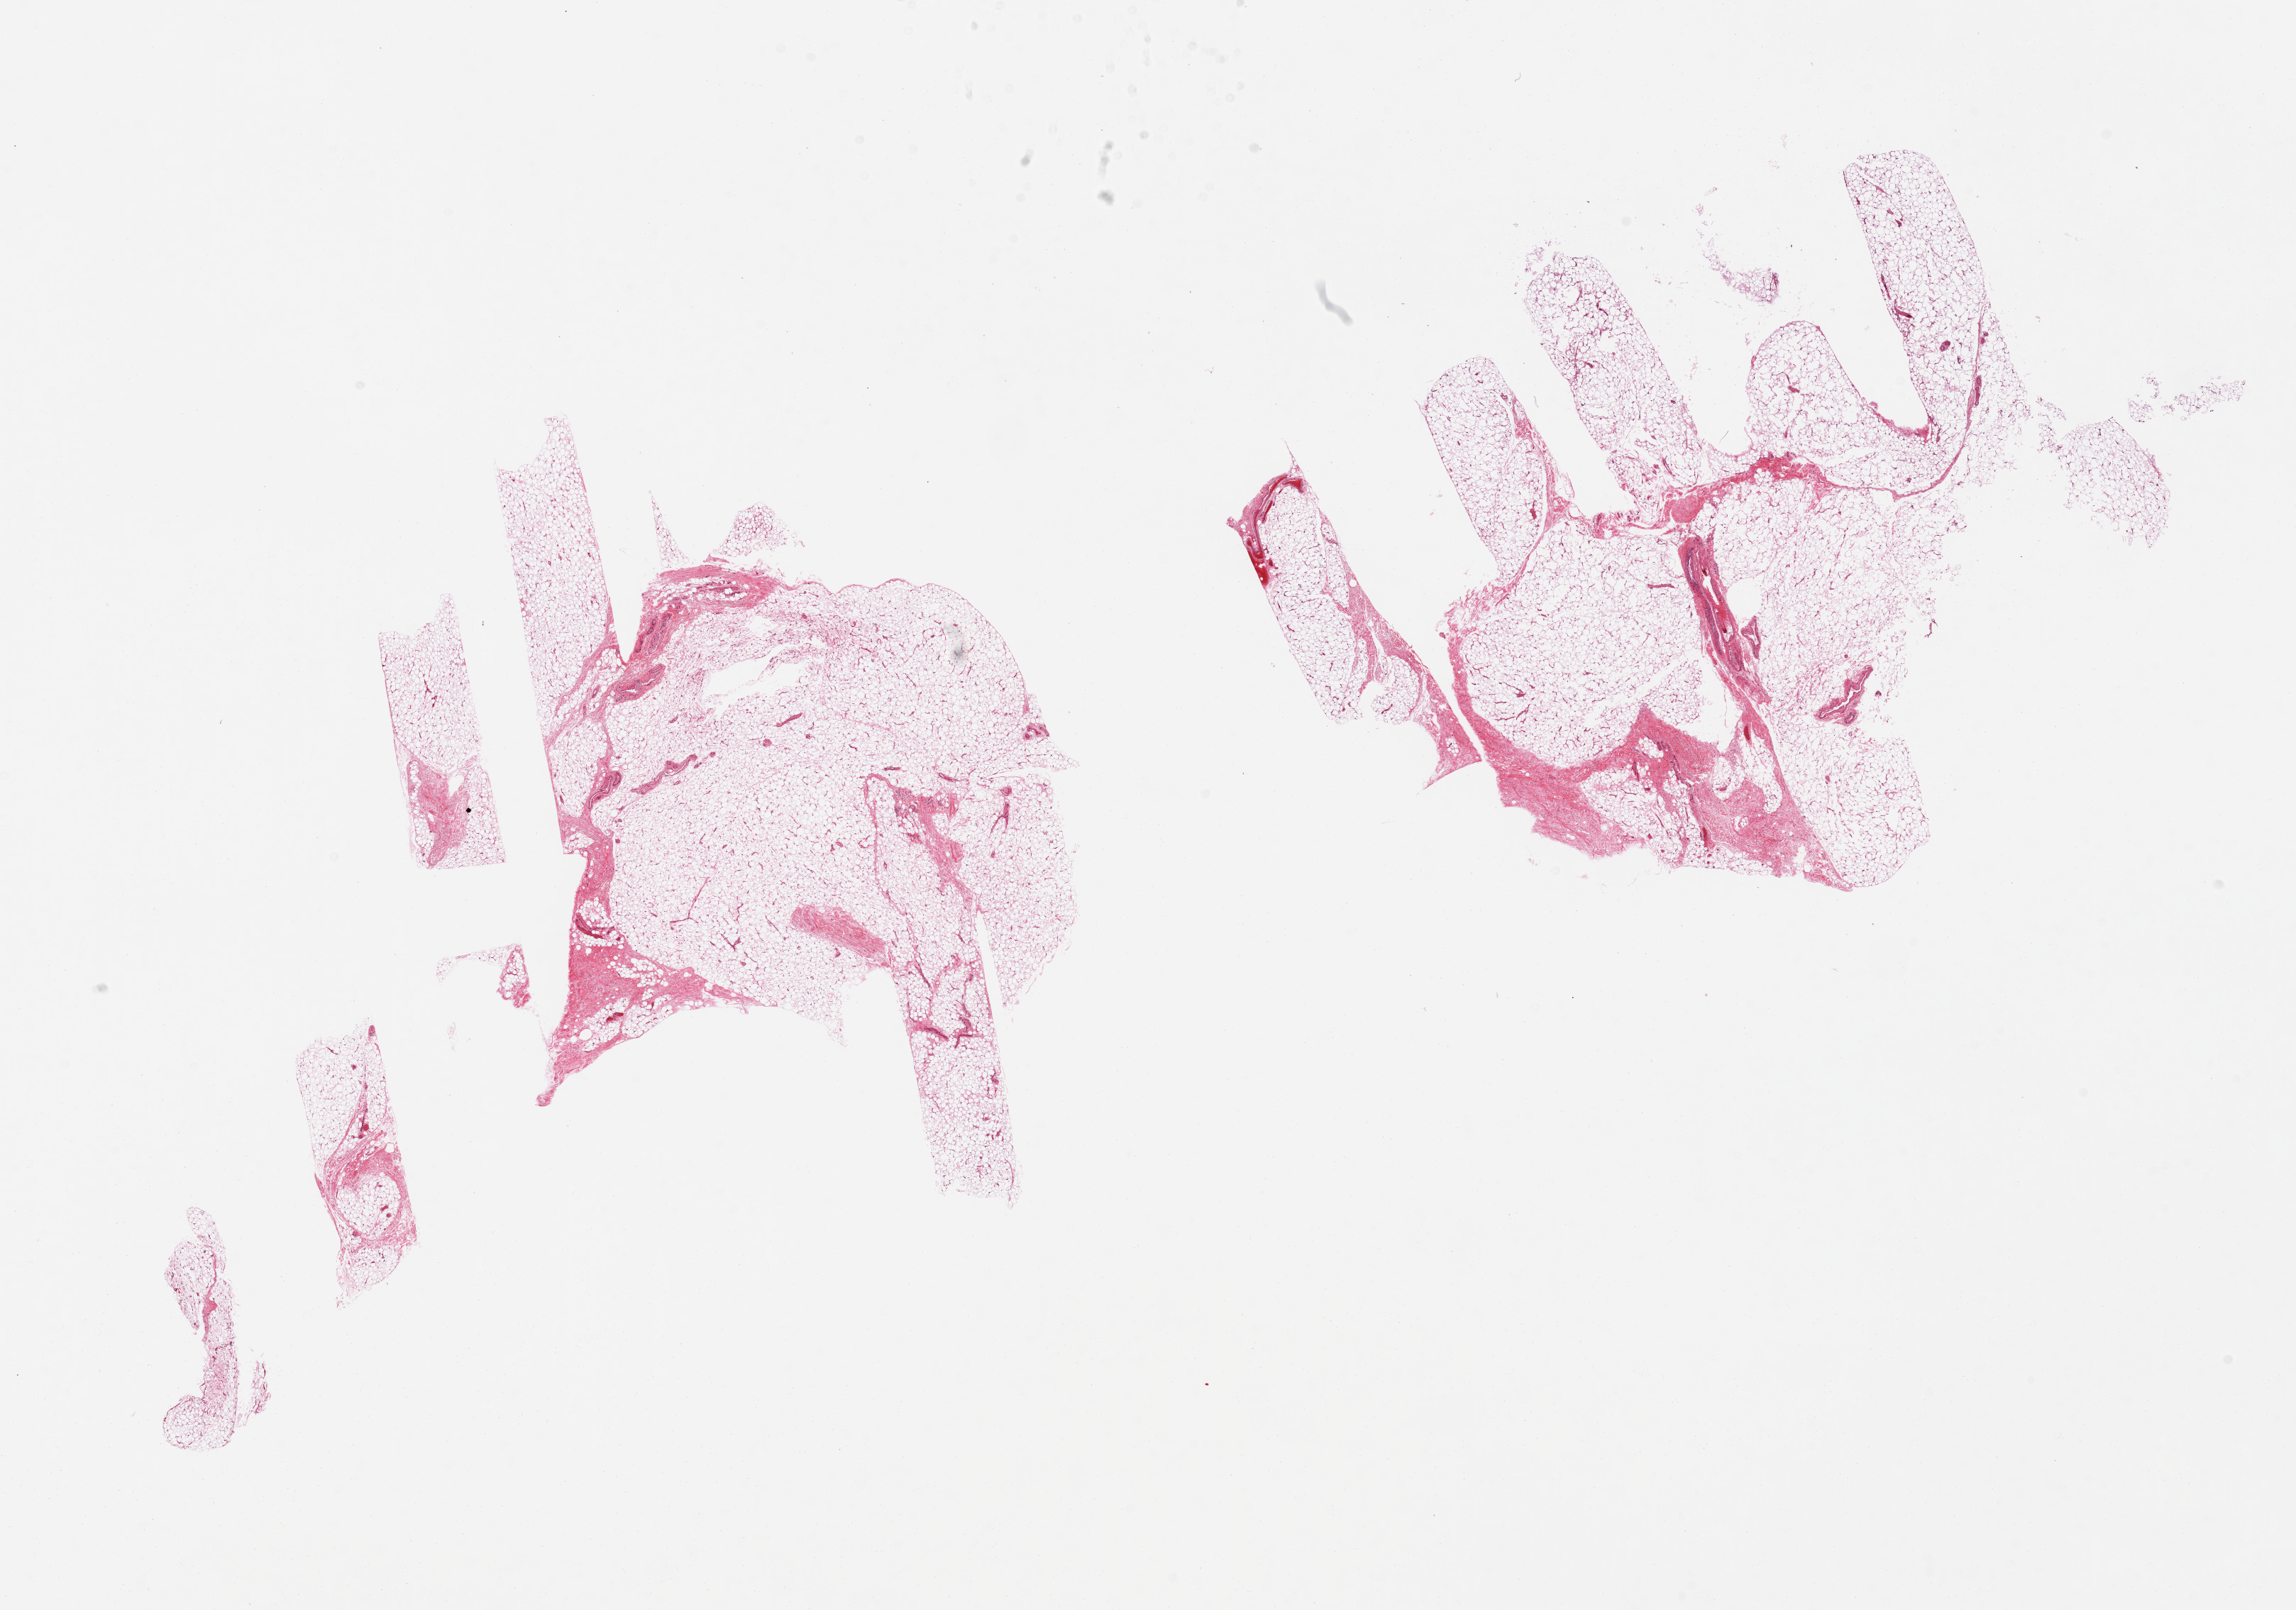
Digitized haematoxylin and eosin-stained section, brightfield — low-resolution overview of the scanned area, about 25.6 x 17.9 mm (acquisition: 20x scan). PAXgene-fixed paraffin-embedded (PFPE) section. Sampled site (target tissue): adipose tissue. Tissue donor sample. Donor: male.
Review note (as recorded): 2 pieces; 10-20% fibro/fascial tissue.